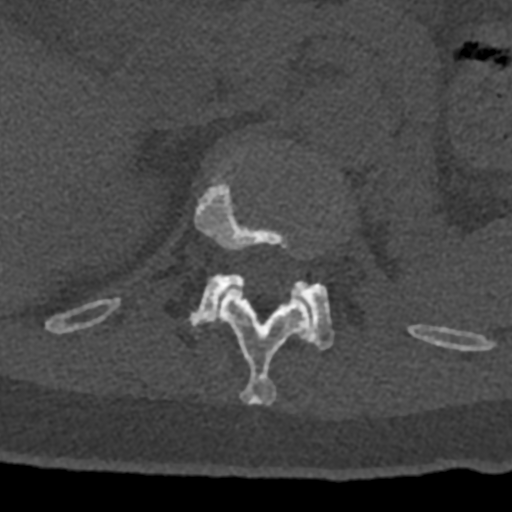
CT including the spine, one axial slice. Position 469 of 797 along the scan axis. Reconstruction kernel Br40s/3. Bone window (W 1800 / L 400 HU). 0.5 mm slice thickness. 512 × 512 image matrix, field of view 160 × 160 mm. Patient: male, 74 years. Case-level facts recorded for this patient, not image findings: primary cancer: renal; vertebrae with lytic lesions (as recorded): T10, L1, L2, L3, L4, L5.
Outlined on this slice (semi-automatic segmentation, software-assisted and operator-edited):
- L1 vertebra: bounding box <189,274,334,350> (left, top, right, bottom; pixels)
- T12 vertebra: <70,162,432,405>